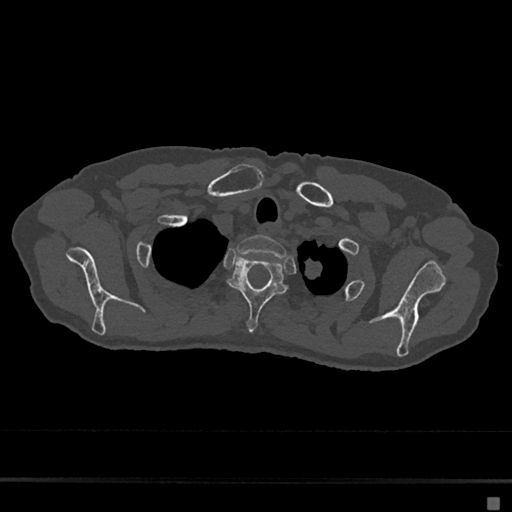
CT including the spine, one axial slice; slice 577 of 797 in the series (ordered by position); reconstruction kernel Br40s/3; bone window (W 1800 / L 400 HU); 0.5 mm slice thickness; 512 × 512 image matrix. Patient: female, 68 years. Case-level facts recorded for this patient, not image findings: primary cancer: renal.
Outlined on this slice (semi-automatically segmented with operator editing):
- T1 vertebra: bounding box (x1, y1, x2, y2) in pixels: (236, 235, 286, 259)
- T2 vertebra: (228, 255, 287, 332)